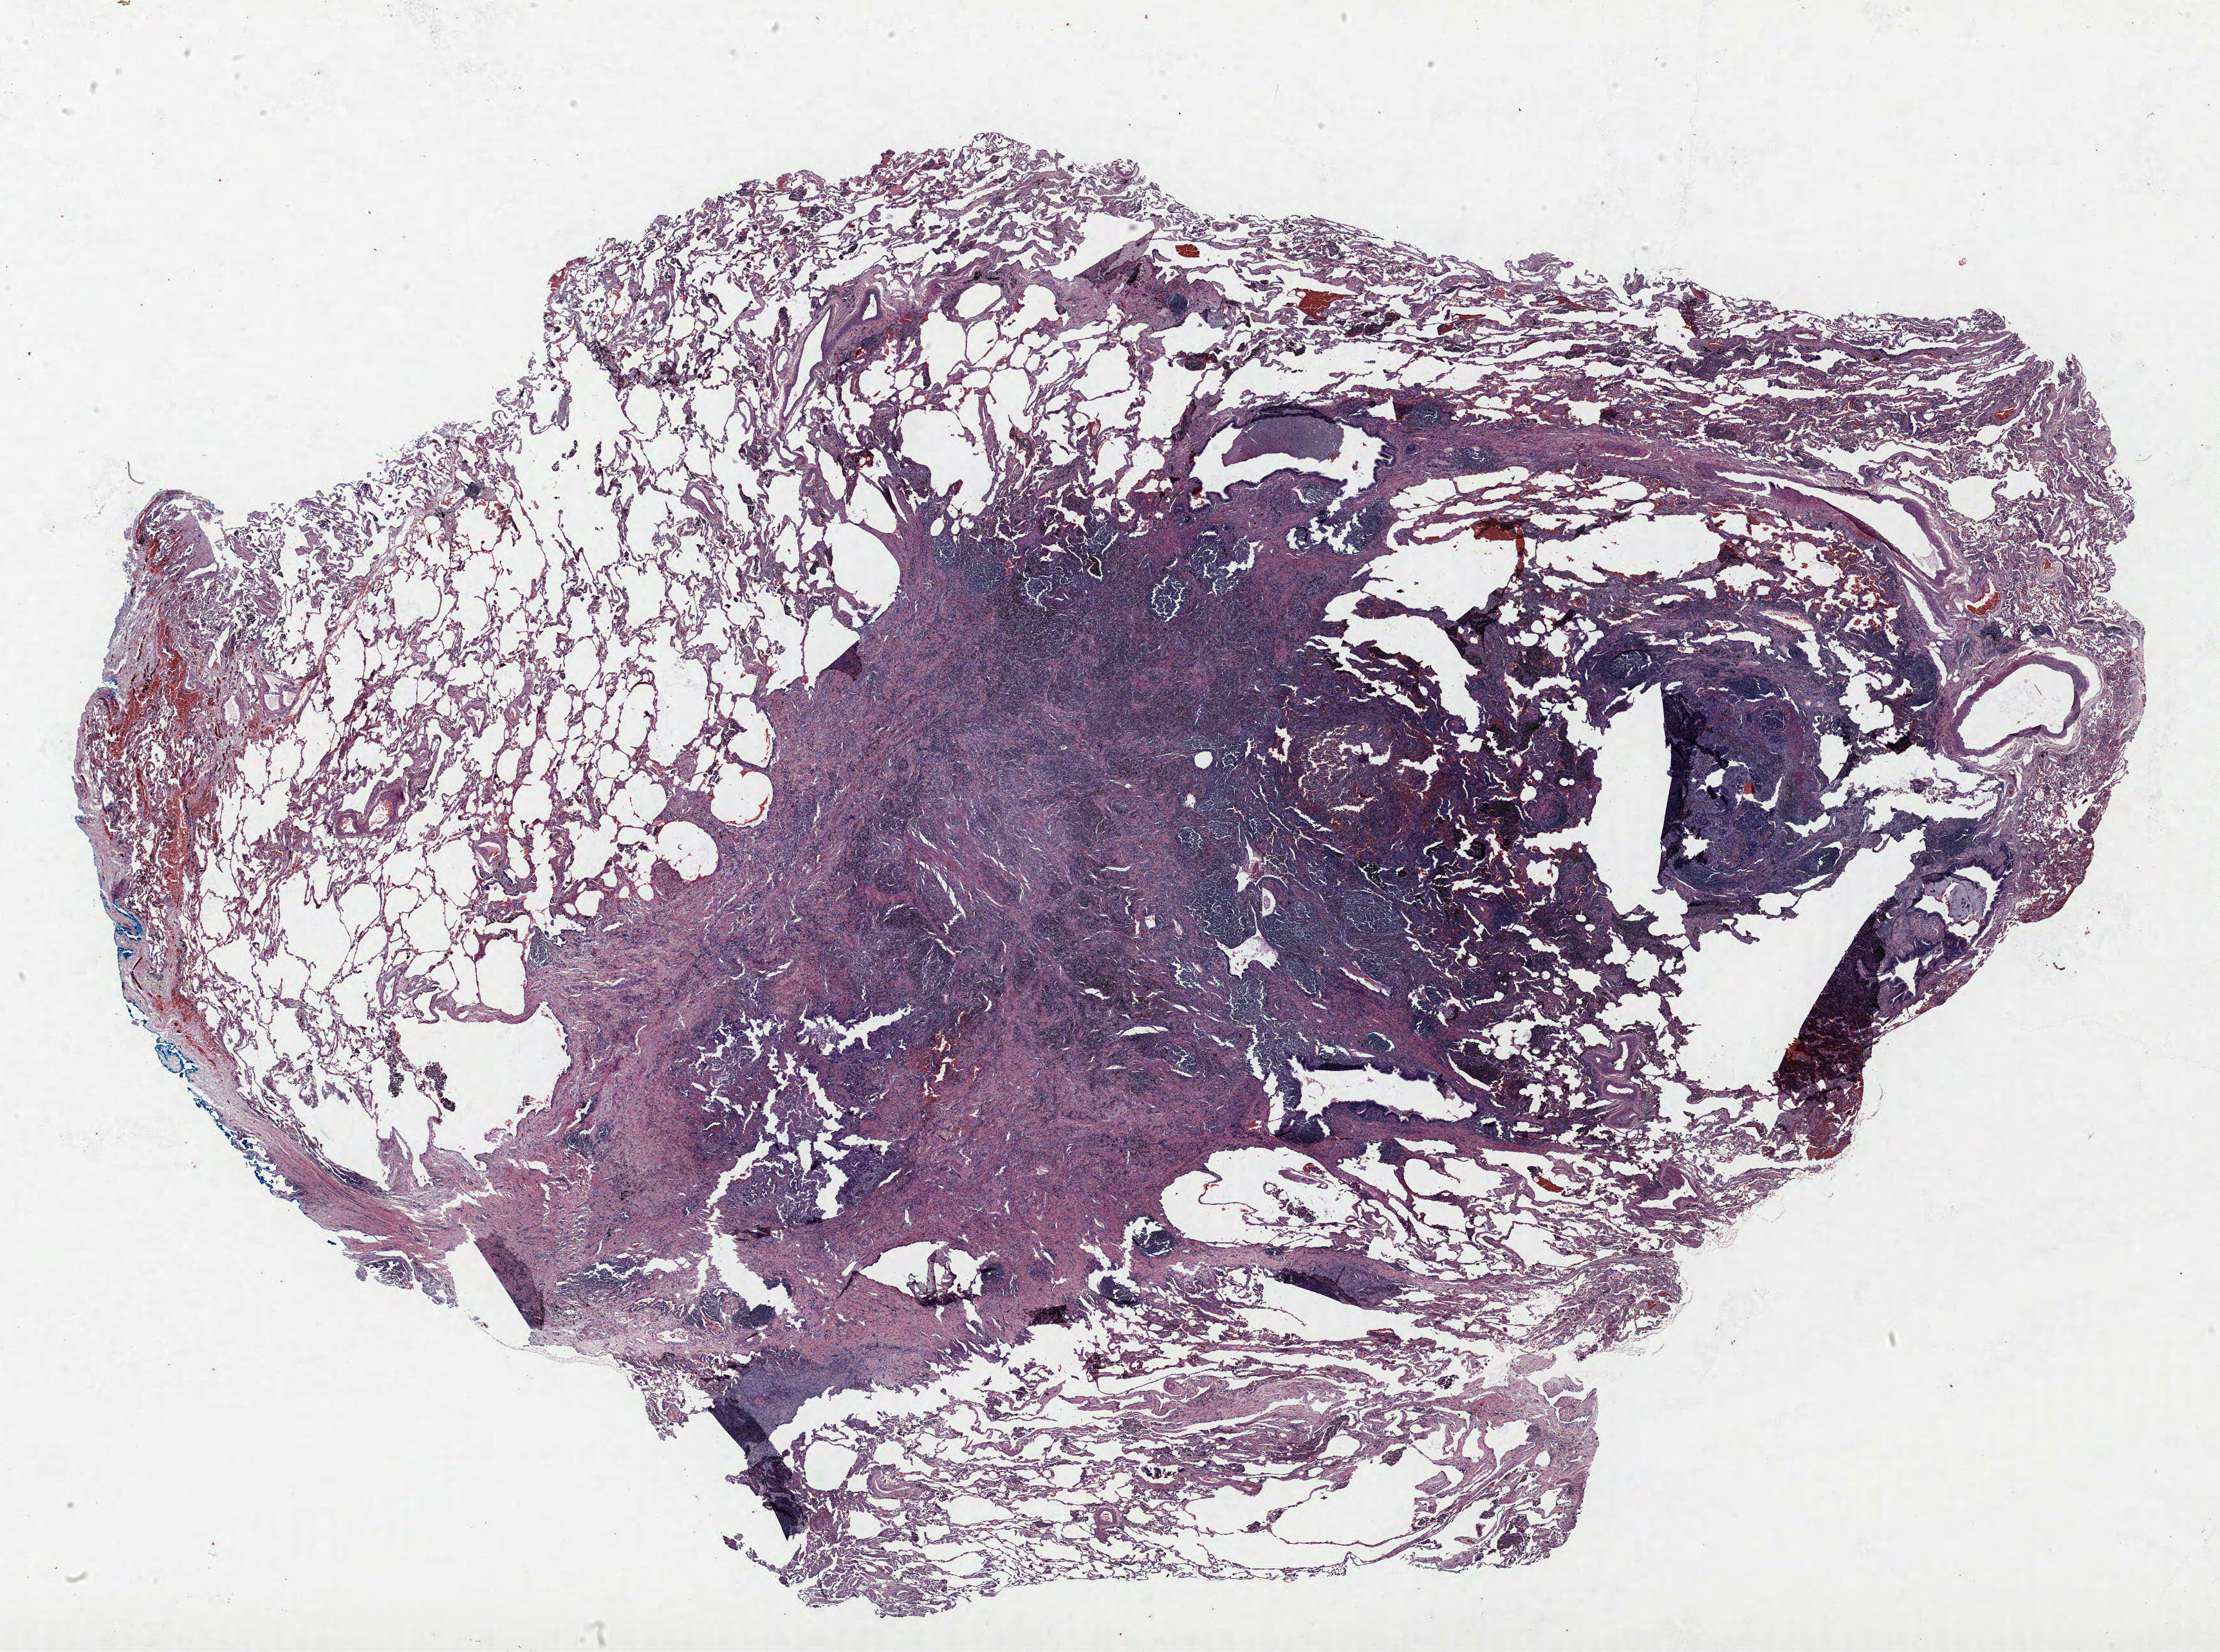
H&E whole-slide image, whole scanned area (about 27.6 x 20.5 mm, slide scanned at 40x) shown as a low-resolution overview; FFPE section; lung tissue. Male, age 67 at enrolment. Grade: poorly differentiated (G3).
- tumour size (pathology): 25 mm
- ICD-O-3 topography: lower lobe of lung (C34.3)
- primary tumour location (clinical record): right lower lobe
- stage (AJCC 6th edition): IA
- participant's lung-cancer diagnosis: Adenocarcinoma, NOS (ICD-O-3 8140/3)